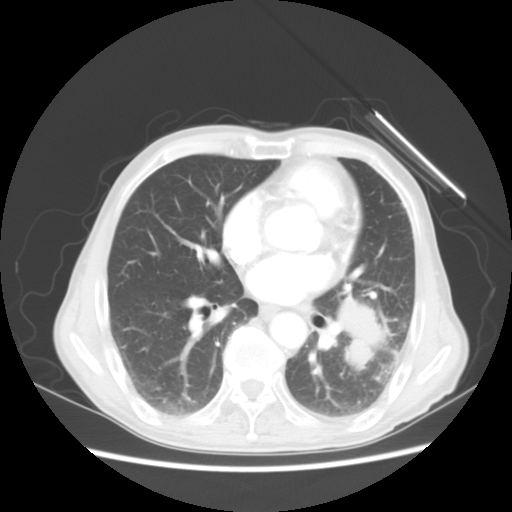
Chest CT, one axial slice; slice 23 of 51 in the series (ordered by position); reconstruction kernel STANDARD; lung window (W 1500 / L -600 HU); 5 mm slice thickness; 512 × 512 image matrix, field of view 360 × 360 mm. Patient: male, 64 years. Case-level facts recorded for this patient, not image findings: clinical TNM (as recorded): T4 N0 M0; histopathological grade: G2-3.
Outlined on this slice (bounding box drawn by a radiologist):
- lung tumour (recorded histology: squamous cell carcinoma): bounding box [x1, y1, x2, y2] px = [331, 283, 382, 368]